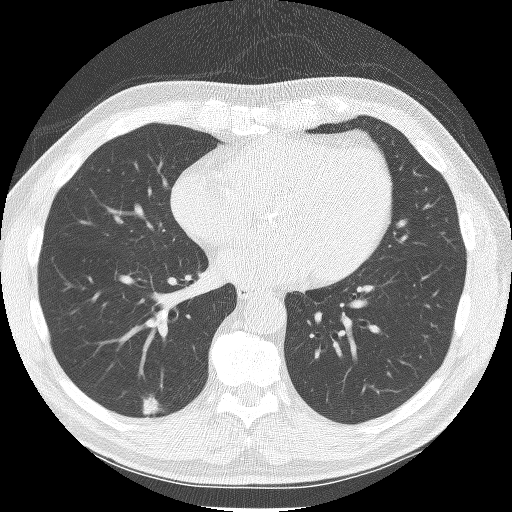
Low-dose screening chest CT, one axial slice. Position 63 of 150 along the scan axis. Reconstruction kernel BONE. 120 kVp. Lung window (W 1500 / L -600 HU). 2.5 mm slice thickness. 512 × 512 image matrix, field of view 335 × 335 mm.
Structures marked on this image (outlined manually by an expert reader):
- lesion 1 (tumor, lower lobe of right lung): bounding box <142,394,159,416> (left, top, right, bottom; pixels)